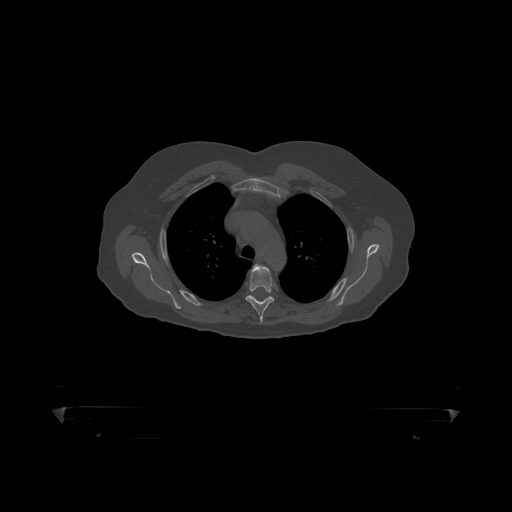
CT including the spine, one axial slice; position 338 of 390 along the scan axis; reconstruction kernel STANDARD; bone window (W 1800 / L 400 HU); 1.25 mm slice thickness; 512 × 512 image matrix, field of view 650 × 650 mm. Patient: male, 60 years. From the clinical record (not read from this slice): primary cancer: prostate.
Structures marked on this image (semi-automatically segmented with operator editing):
- T4 vertebra: bounding box (x1, y1, x2, y2) in pixels: (246, 264, 275, 319)